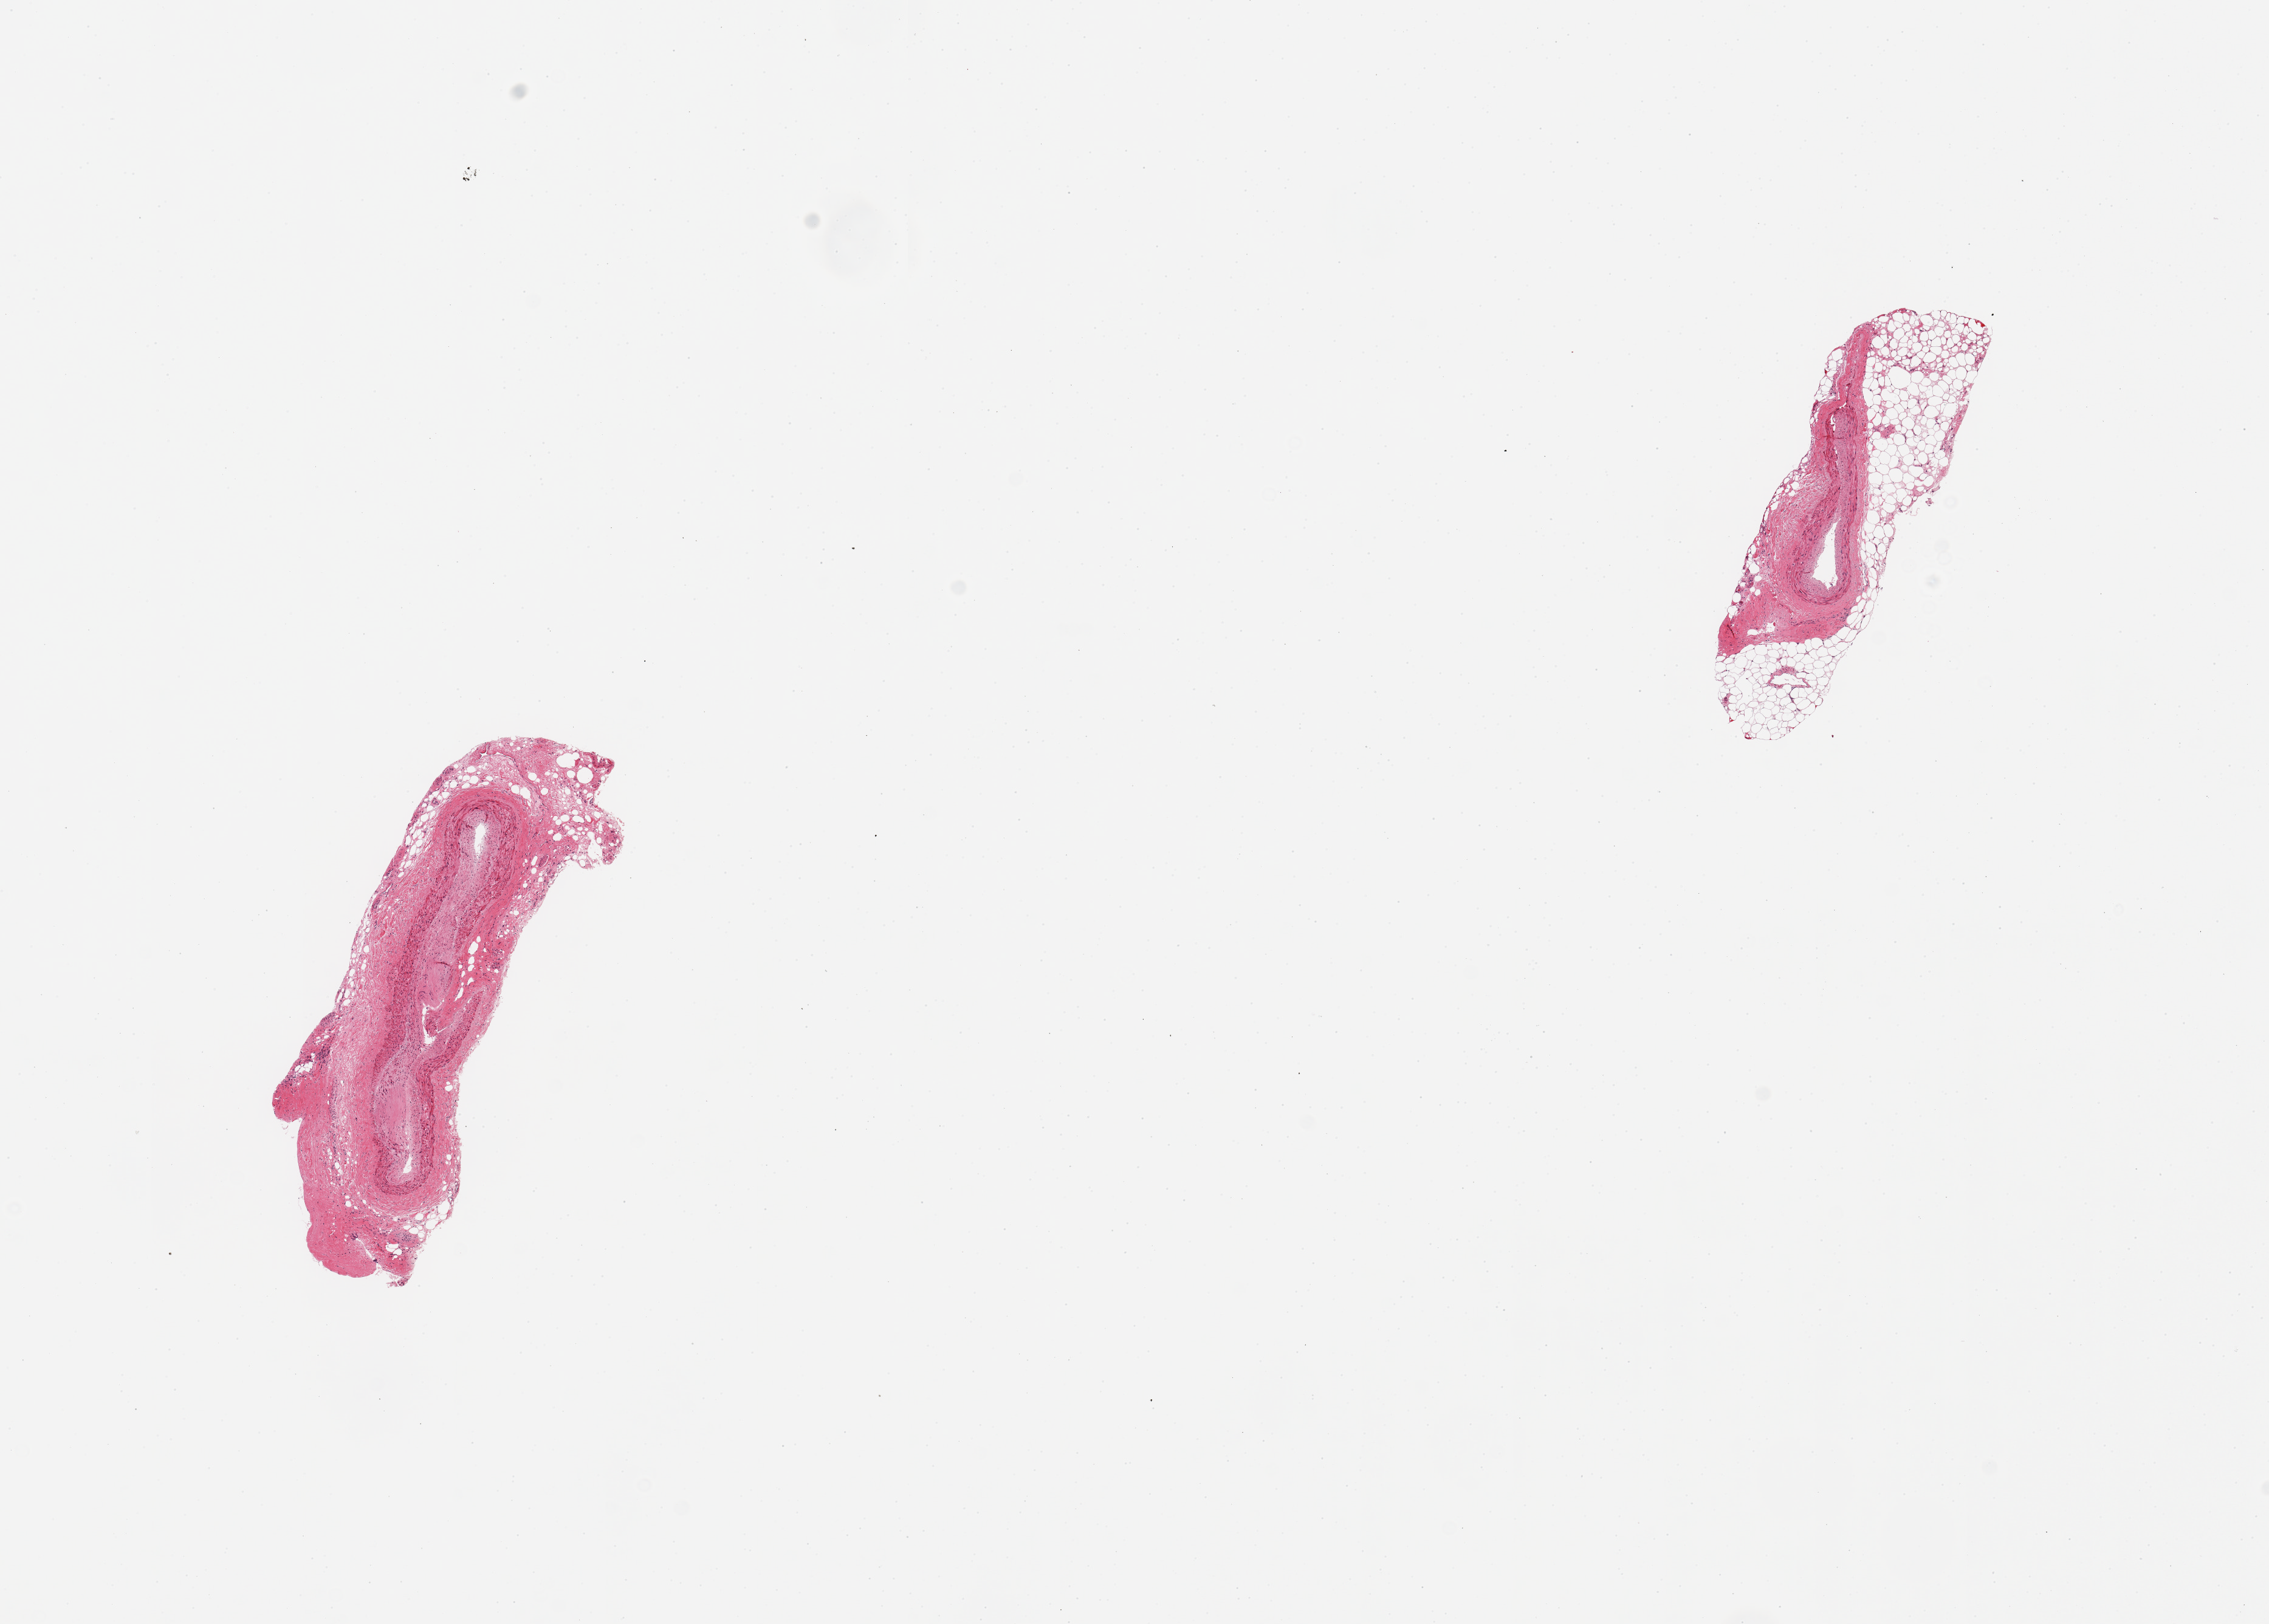
Hematoxylin and eosin (H&E) whole-slide image, low-resolution overview of the scanned area, about 14.8 x 10.6 mm (slide scanned at 20x). PAXgene-fixed paraffin-embedded (PFPE) section. Target tissue: coronary artery. Tissue donor sample.
Review note (as recorded): 2 pieces; focall plaques; 50% & 10% external fat.